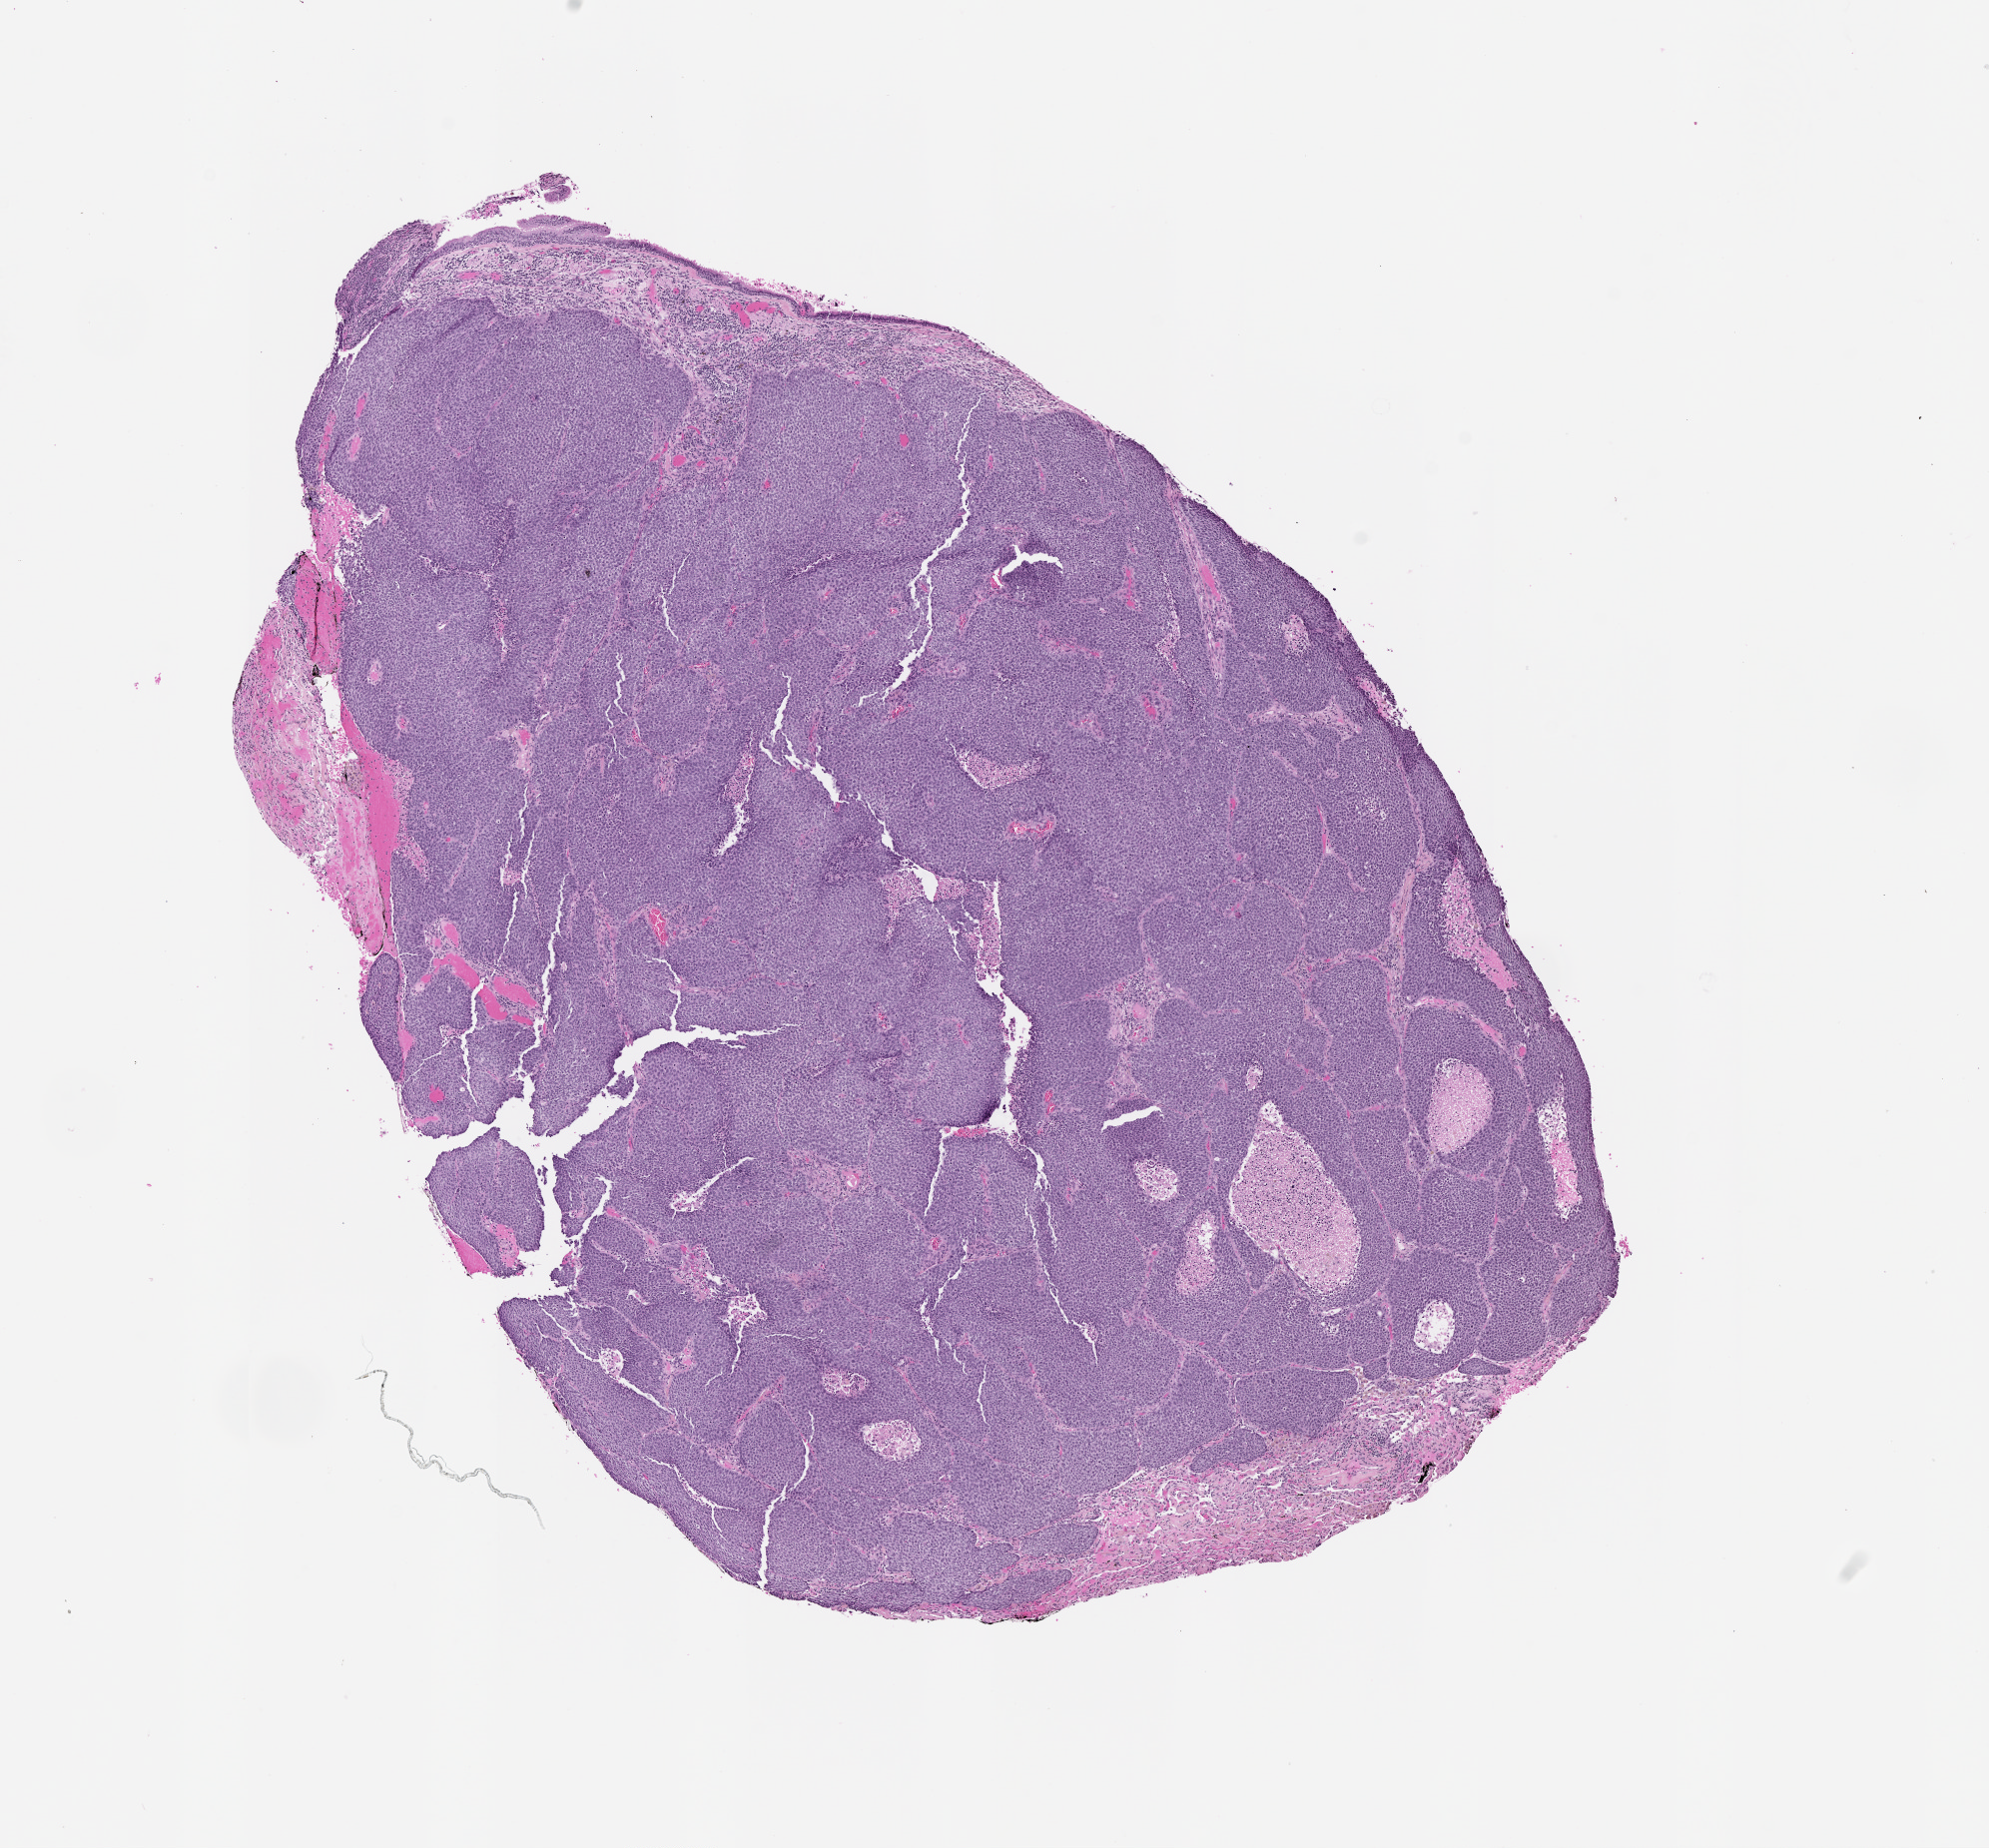
Hematoxylin and eosin (H&E) stained whole-slide image — shown as a low-resolution overview of the whole scanned area (about 8.0 x 7.4 mm, acquisition: 20x scan). Lung, tumour tissue. 68-year-old male patient.
Patient diagnosis (cohort enrolment): squamous cell carcinoma (lung).